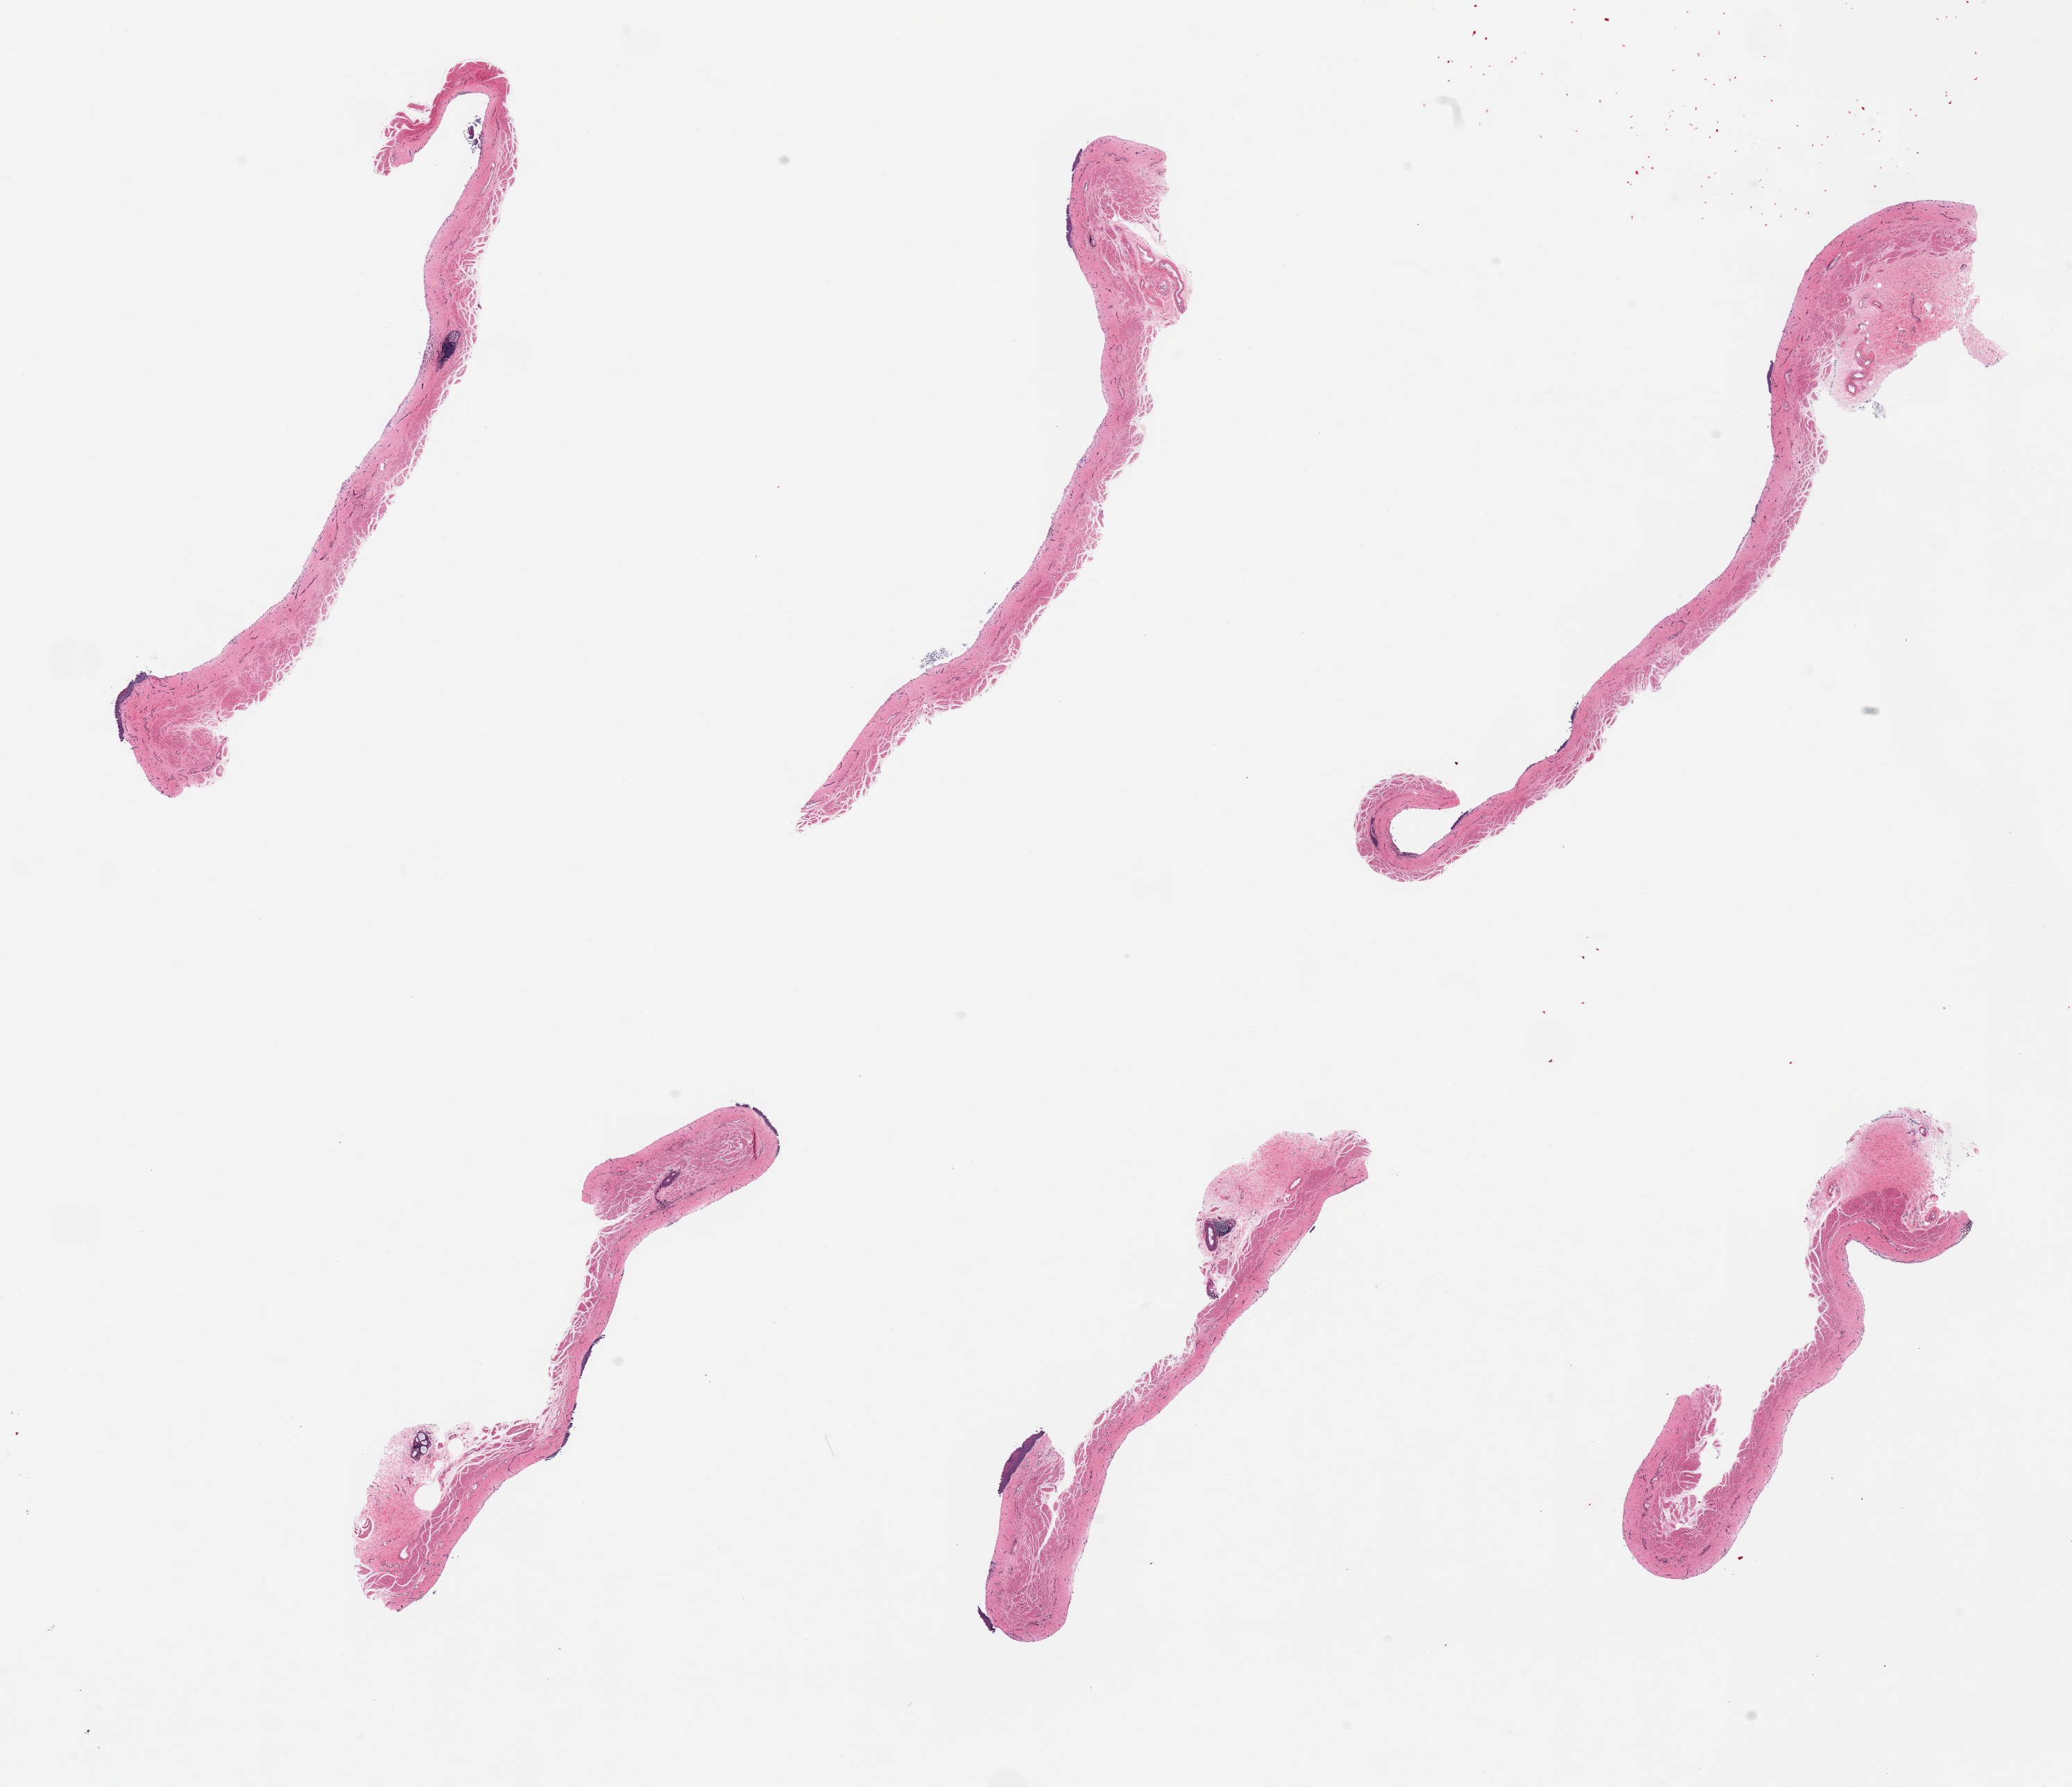
H&E whole-slide image — a low-resolution overview of the entire scanned area, about 23.6 x 20.4 mm; PAXgene-fixed, paraffin-embedded tissue; sampled site (target tissue): esophageal mucous membrane; tissue donor sample. Donor sex: male.
Review note (as recorded): 6 pieces; epithelium almost totally sloughed.